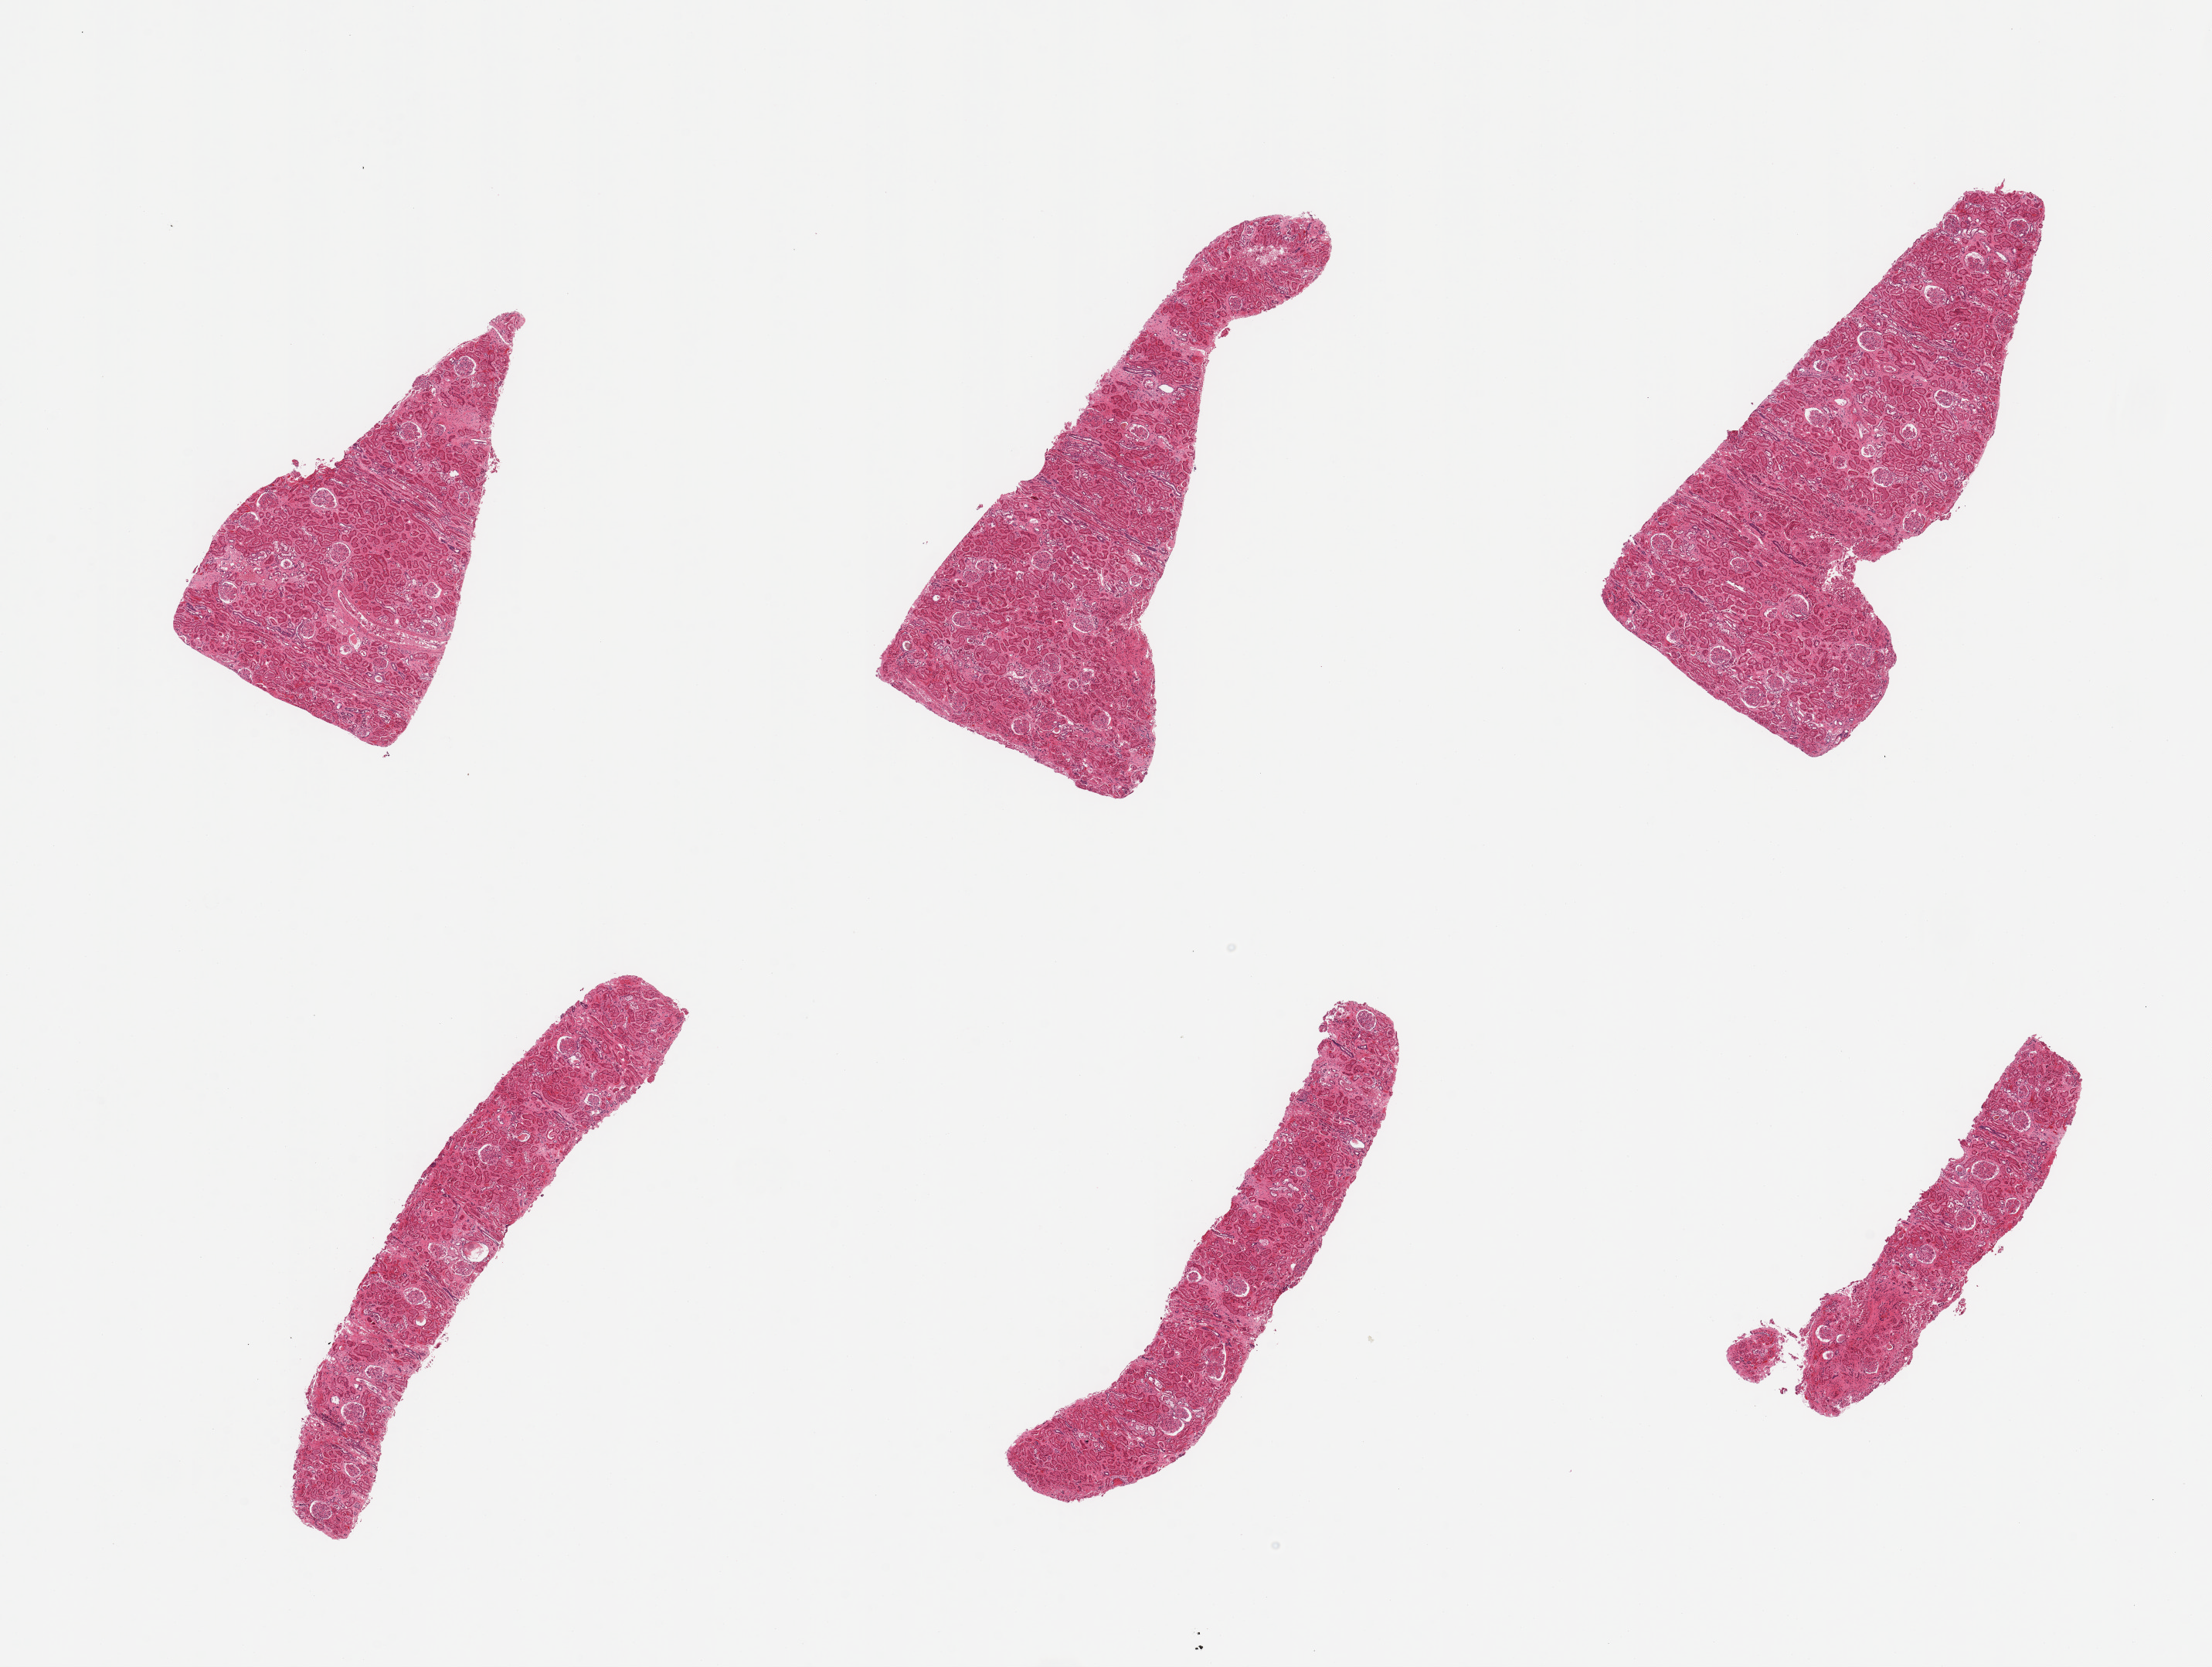
Digitized H&E-stained section, brightfield — a low-resolution overview of the entire scanned area, about 22.6 x 17.1 mm (from a 20x scan); PAXgene-fixed, paraffin-embedded tissue; section of renal cortex (target tissue); donor tissue sample. Donor: male.
Reviewer comment on this tissue sample: 6 pieces; no acute or chronic lesions.